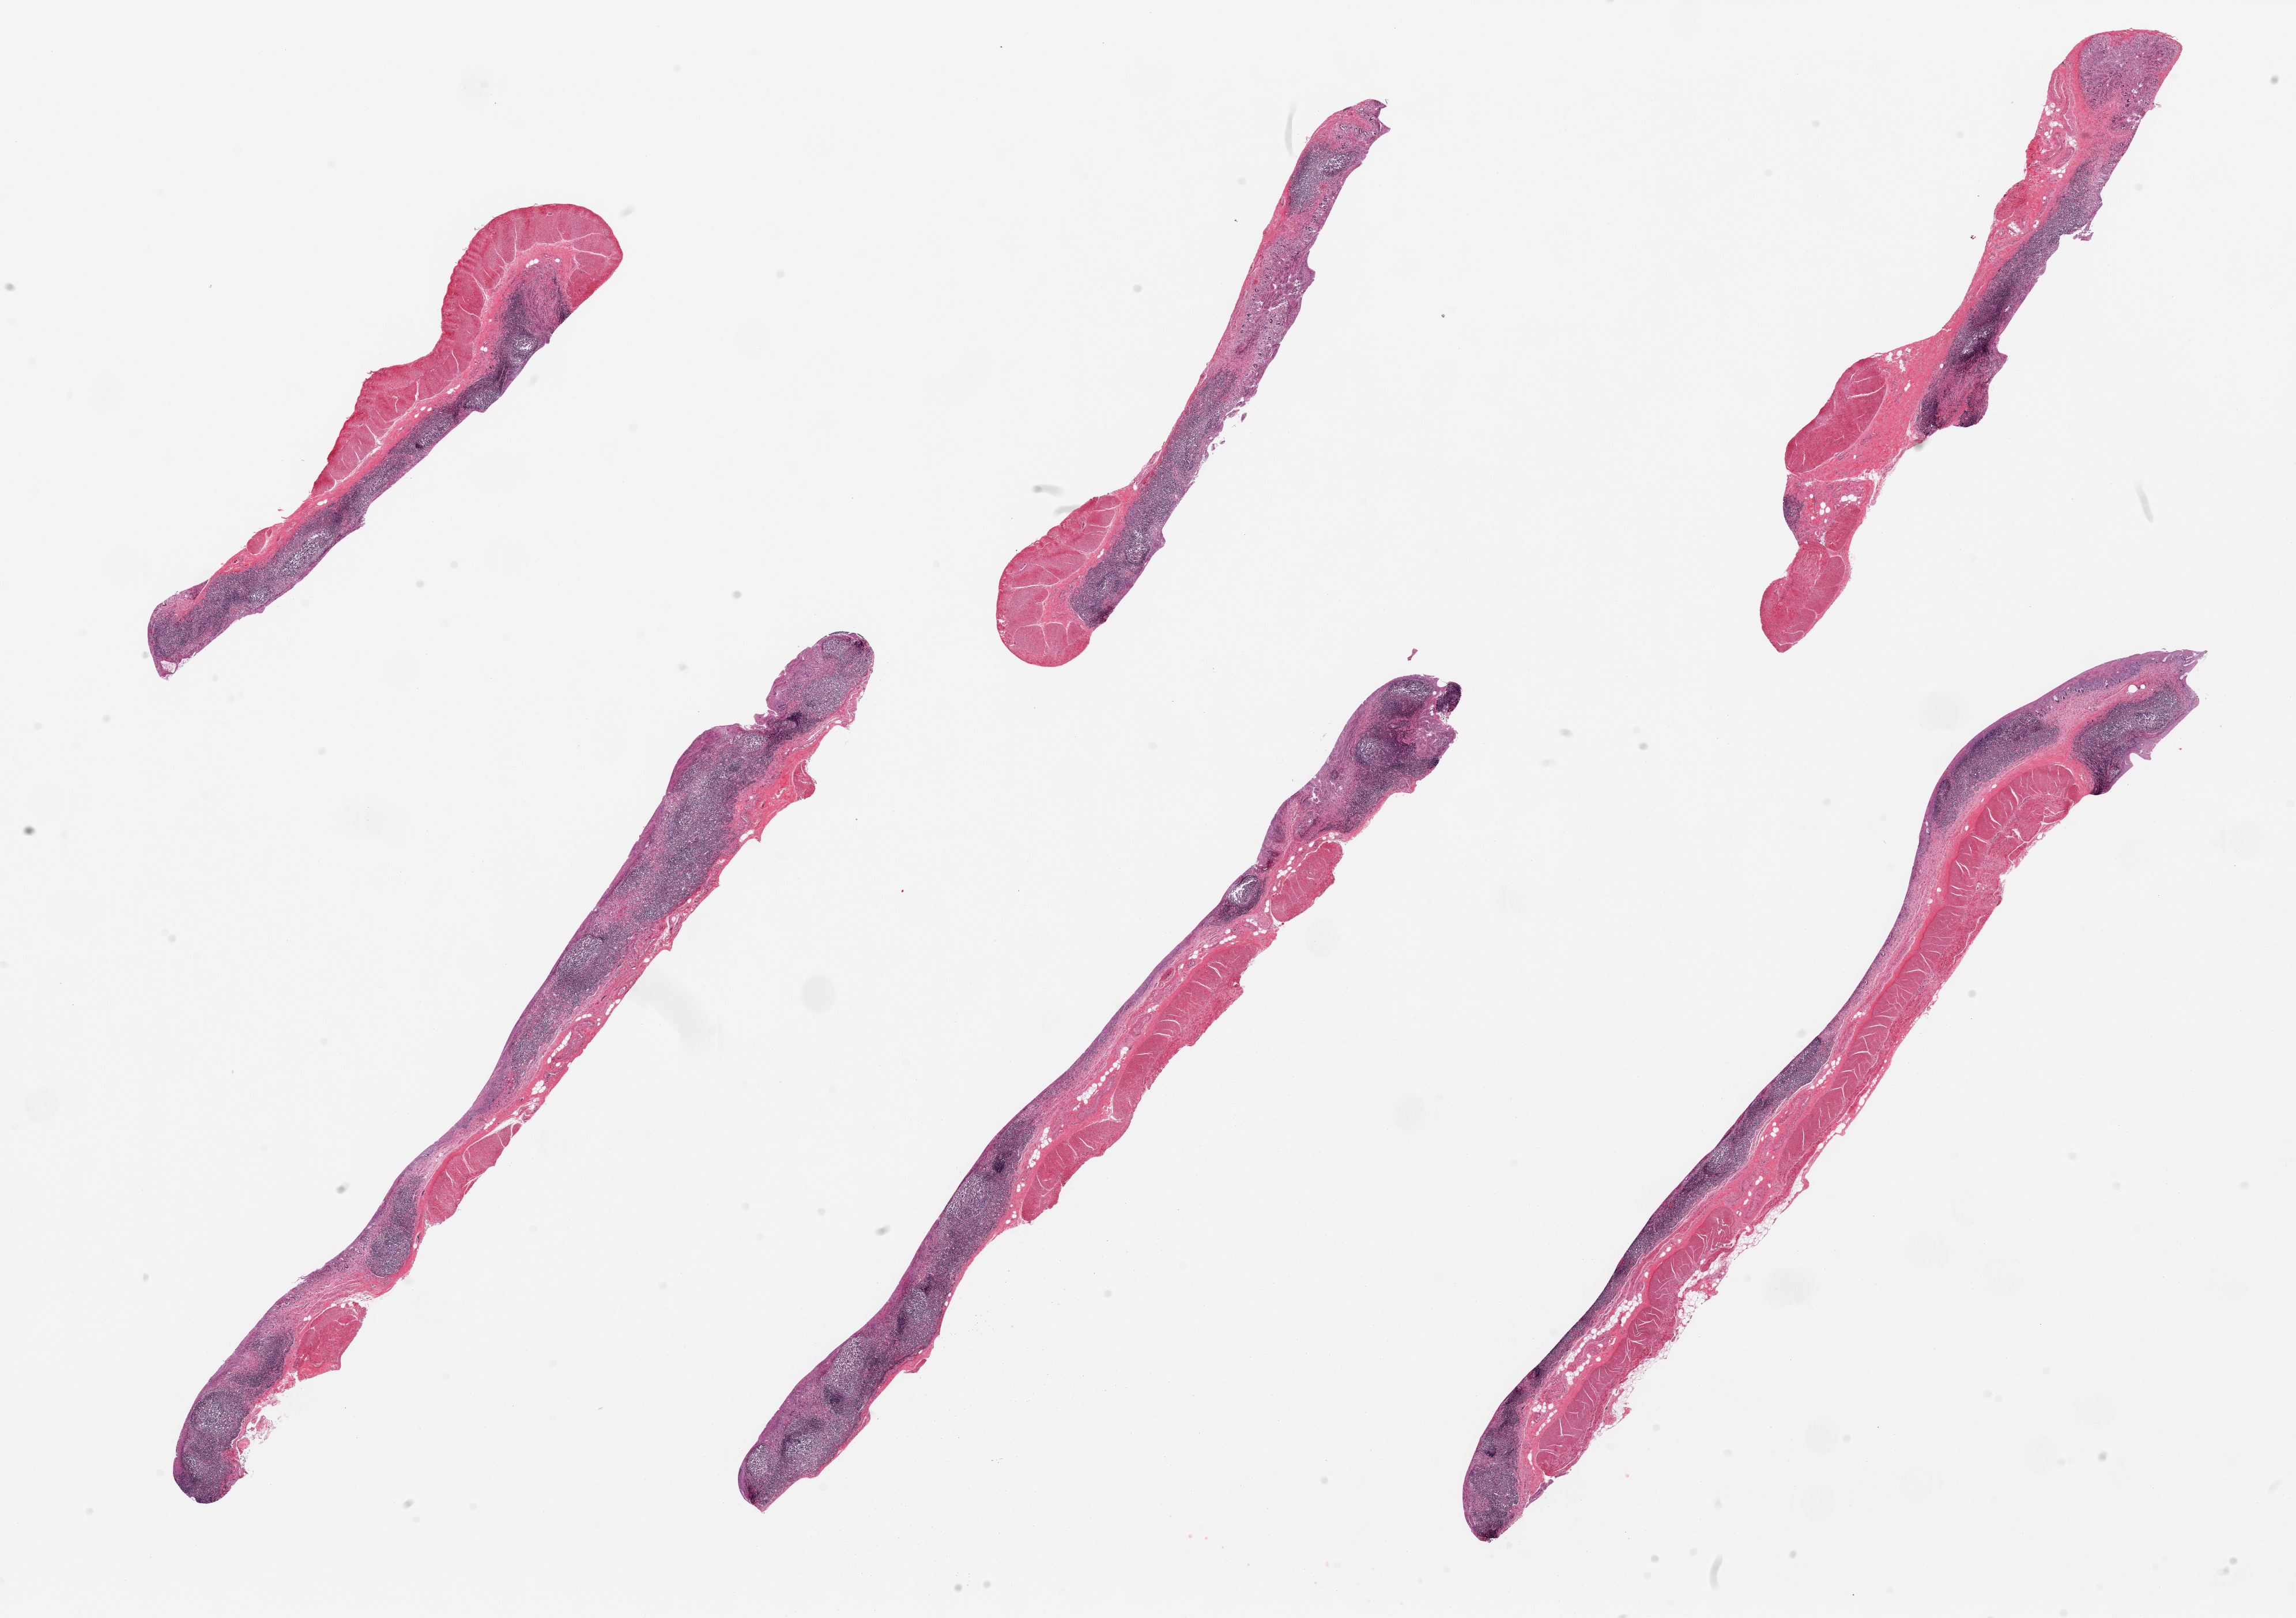
Whole-slide image, hematoxylin and eosin (H&E) stain, low-resolution overview of the scanned area, about 31.5 x 22.2 mm. PAXgene-fixed, paraffin-embedded tissue. Target tissue: ileum. Donor tissue sample.
Review note (as recorded): 6 pieces; mucosa totally autolyzed, but abundant lymphoid tissue remains in all pieces.